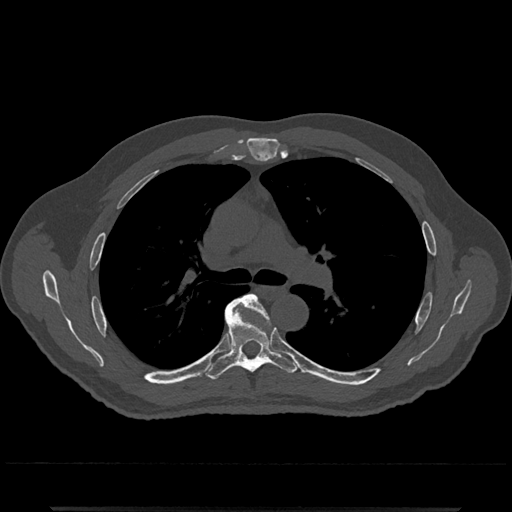
CT including the spine, one axial slice; position 787 of 797 along the scan axis; reconstruction kernel Br40s/3; 120 kVp; bone window (W 1800 / L 400 HU); 0.5 mm slice thickness; 512 × 512 image matrix, field of view 393 × 393 mm. Male patient, age 67 years. Case-level facts recorded for this patient, not image findings: primary cancer: prostate.
Outlined on this slice (semi-automatically segmented with operator editing):
- T5 vertebra: bounding box (x1, y1, x2, y2) in pixels: (234, 294, 269, 319)
- T6 vertebra: (205, 299, 298, 380)